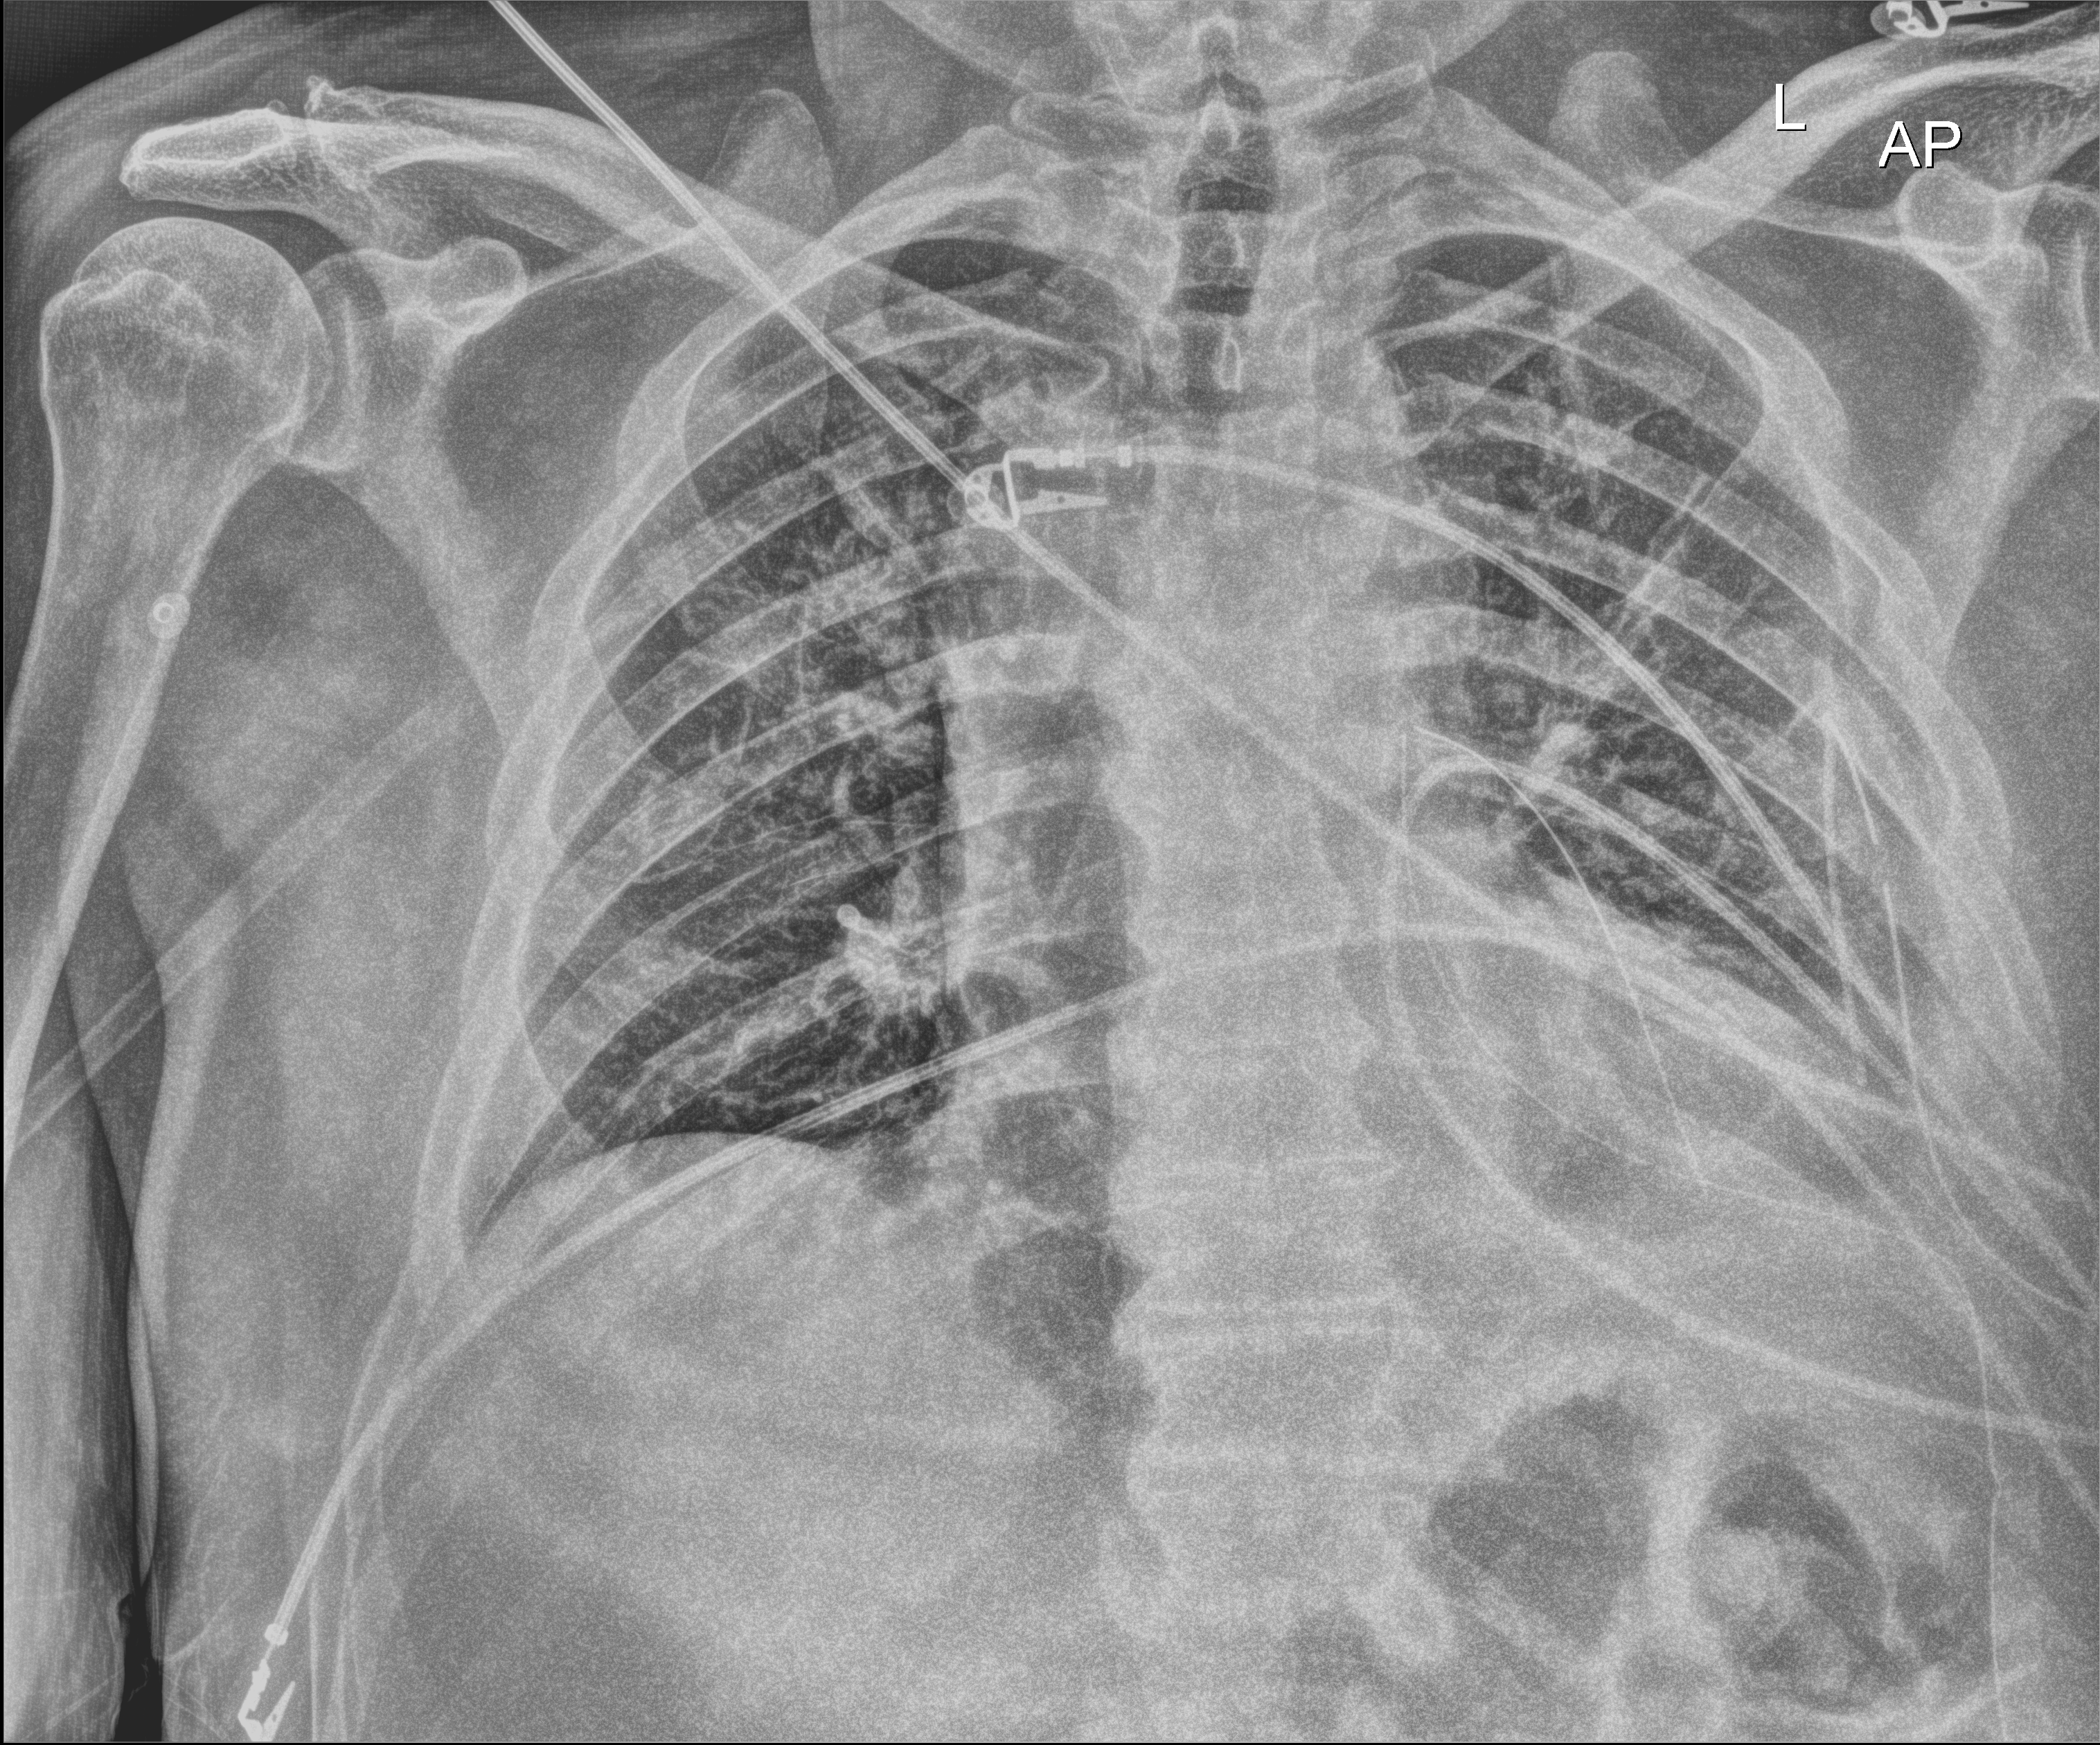
Portable chest radiograph; anteroposterior (AP) projection. Male patient hospitalised with COVID-19, age 18–59 years.
Hospital-stay facts (about this admission, not read from this image; timing relative to this image not recorded): length of hospital stay: 10 days.